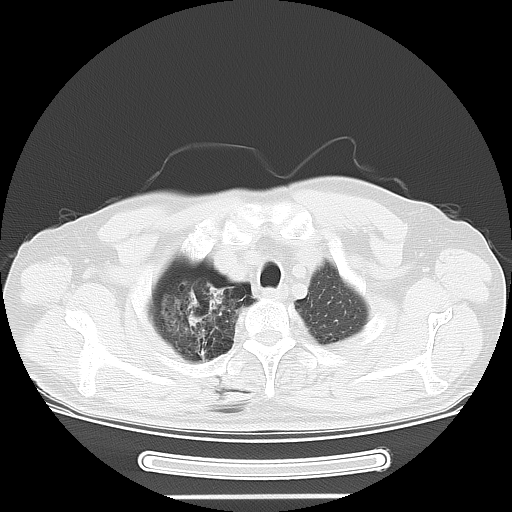
Chest CT, one axial slice; slice 51 of 57 in the series (ordered by position); 120 kVp; lung window (W 1500 / L -600 HU); 5 mm slice thickness; 512 × 512 image matrix. Patient: male, 61 years. Case-level facts recorded for this patient, not image findings: clinical TNM (as recorded): T1c N3 M1b.
Structures marked on this image (bounding box drawn by a radiologist):
- lung tumour (recorded histology: adenocarcinoma): bounding box [x1, y1, x2, y2] px = [161, 278, 240, 360]